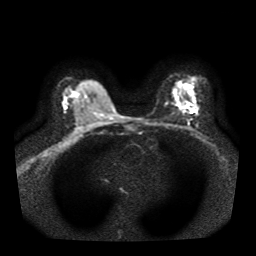
Breast MRI, one axial slice; slice 24 of 41 in the series (ordered by position); diffusion-weighted series; image 2 of 4 stored at this slice position (different b-values; order by instance number); 1.5 T; 5 mm slice thickness; 256 × 256 image matrix. Female patient.
Structures marked on this image (expert manual segmentation):
- tumour on diffusion-weighted imaging: bounding box <183,102,192,107> (left, top, right, bottom; pixels)